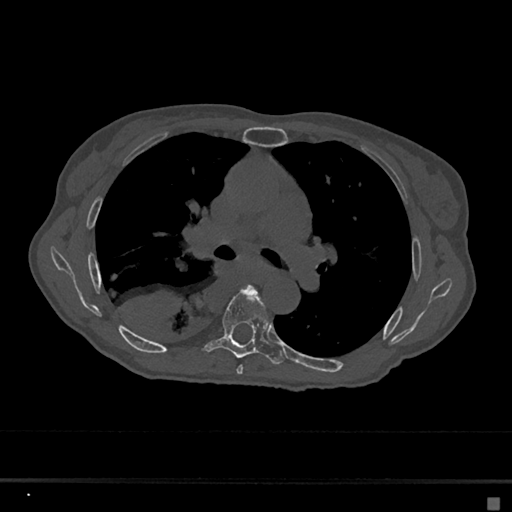
CT including the spine, one axial slice; slice 425 of 797 in the series (ordered by position); reconstruction kernel Br40s/3; 120 kVp; bone window (W 1800 / L 400 HU); 0.5 mm slice thickness; 512 × 512 image matrix, field of view 360 × 360 mm. Female patient, age 68 years. Case-level facts recorded for this patient, not image findings: primary cancer: renal.
Structures marked on this image (semi-automatic segmentation, software-assisted and operator-edited):
- T5 vertebra: bounding box <236,286,260,375> (left, top, right, bottom; pixels)
- T6 vertebra: <204,286,284,365>